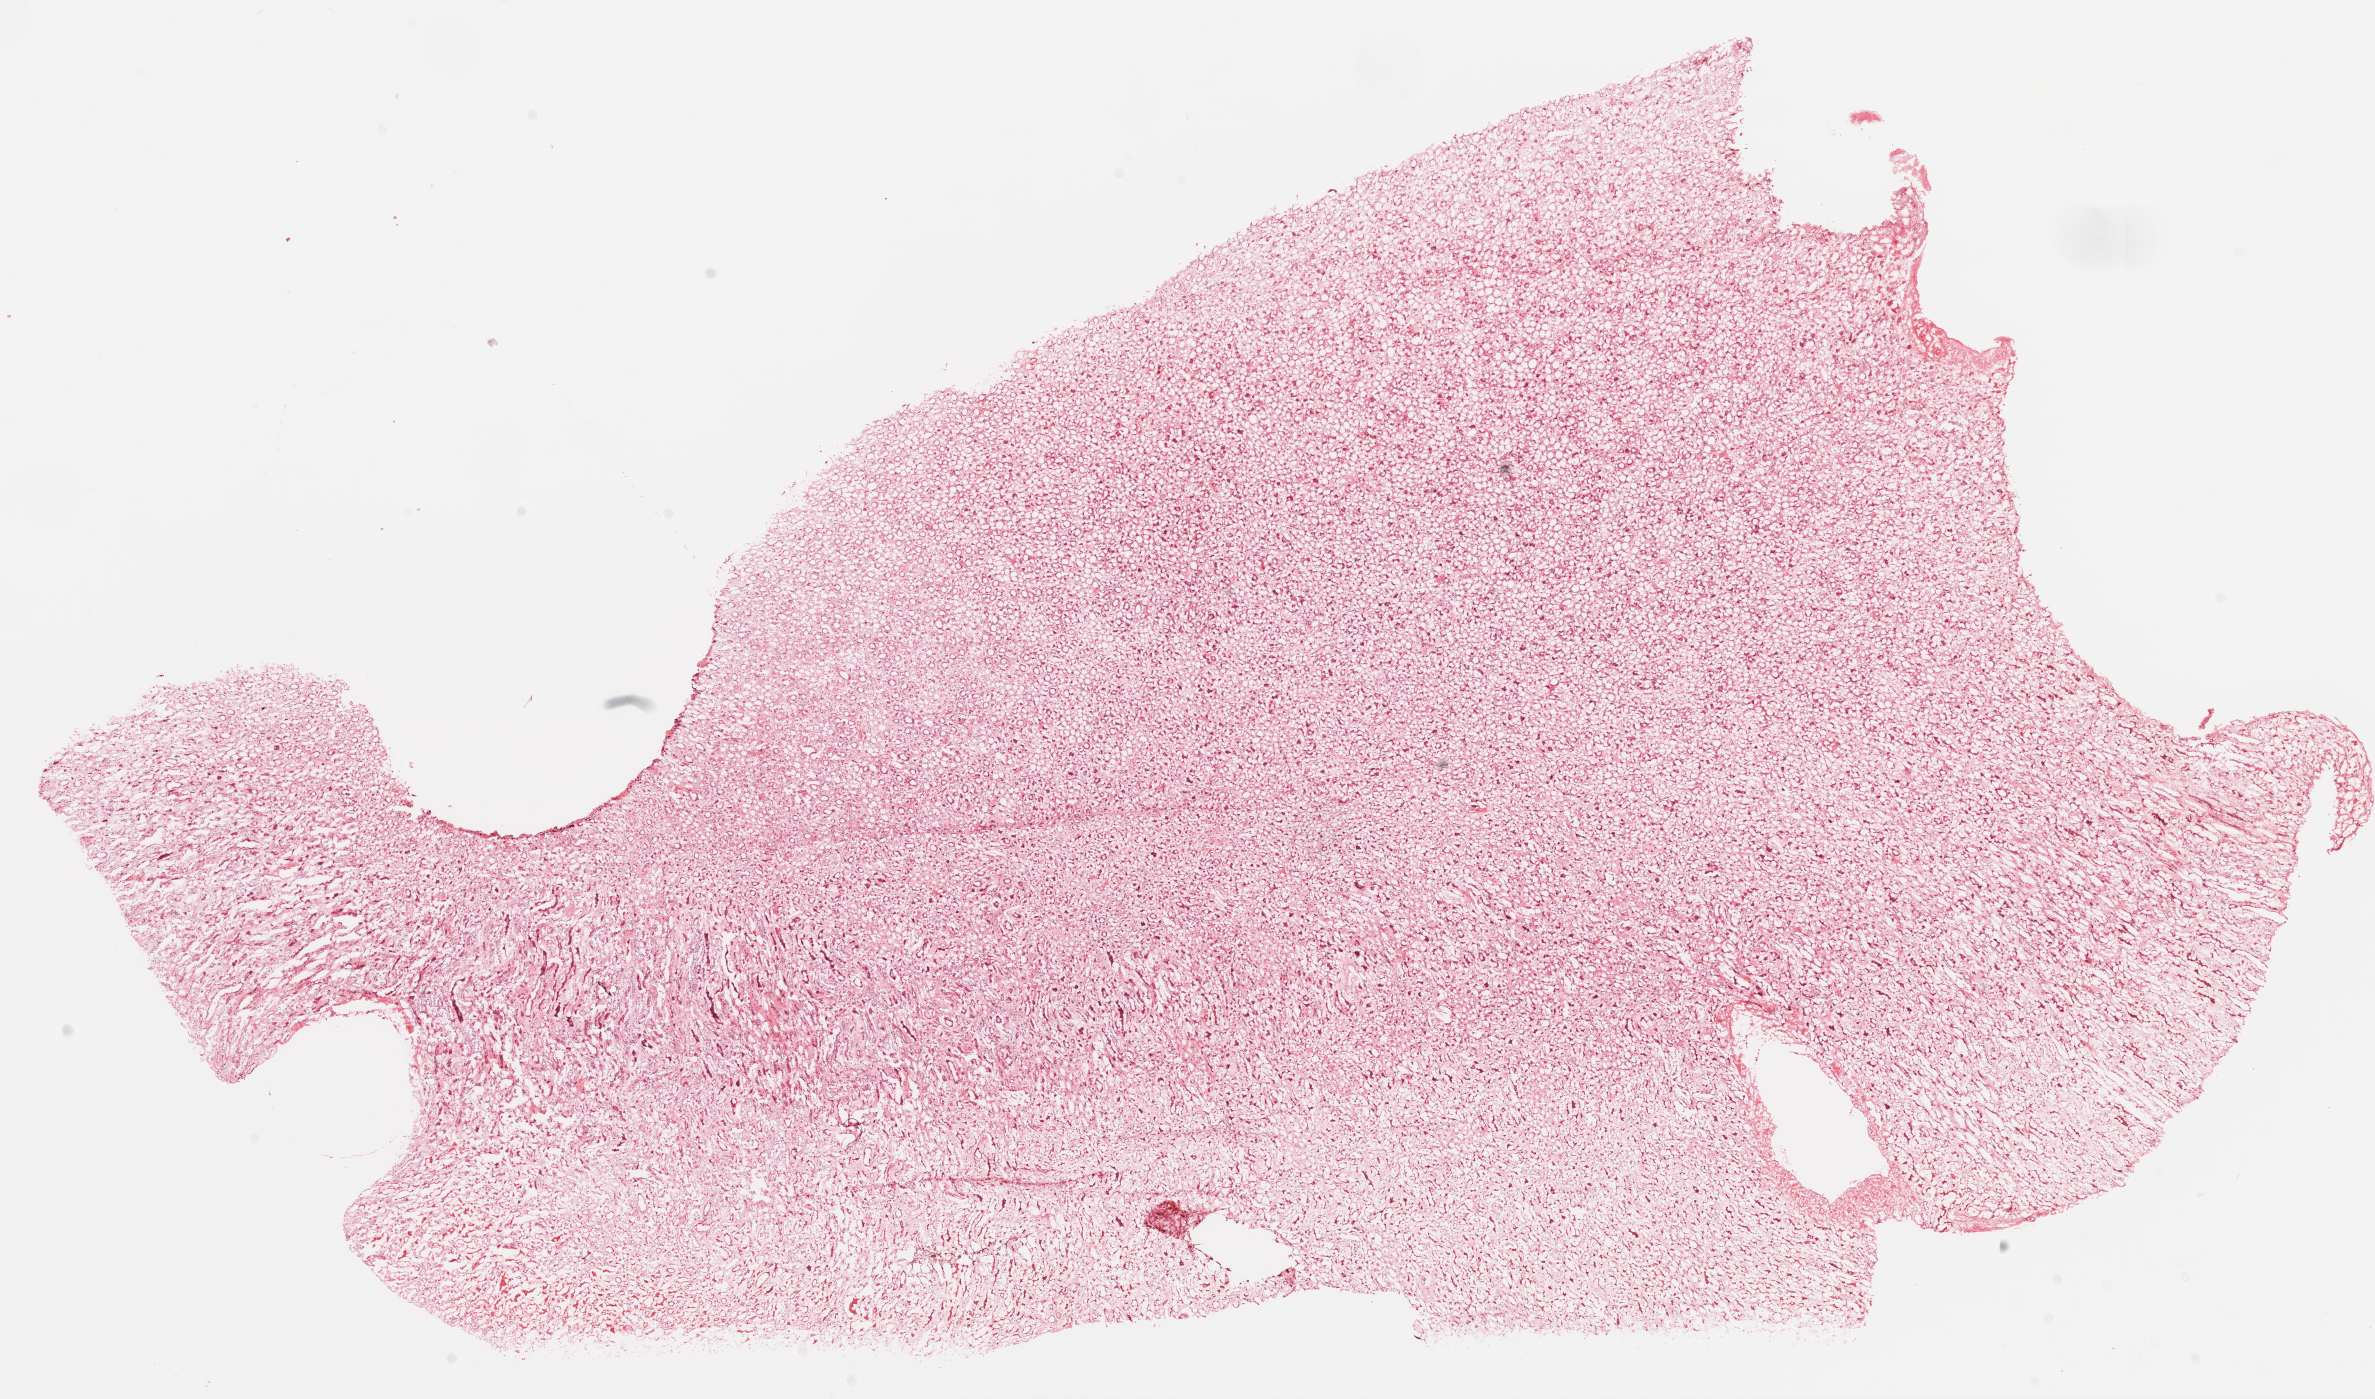
Hematoxylin and eosin (H&E) stained whole-slide image — shown as a low-resolution overview of the whole scanned area (about 19.1 x 11.2 mm). Frozen section from the top of the tissue portion. Kidney, solid tissue normal (non-tumour tissue) sample. Male, age 63 years at initial diagnosis.
This section: solid tissue normal sample (biorepository sample class). Patient diagnosis: Clear cell adenocarcinoma, NOS.